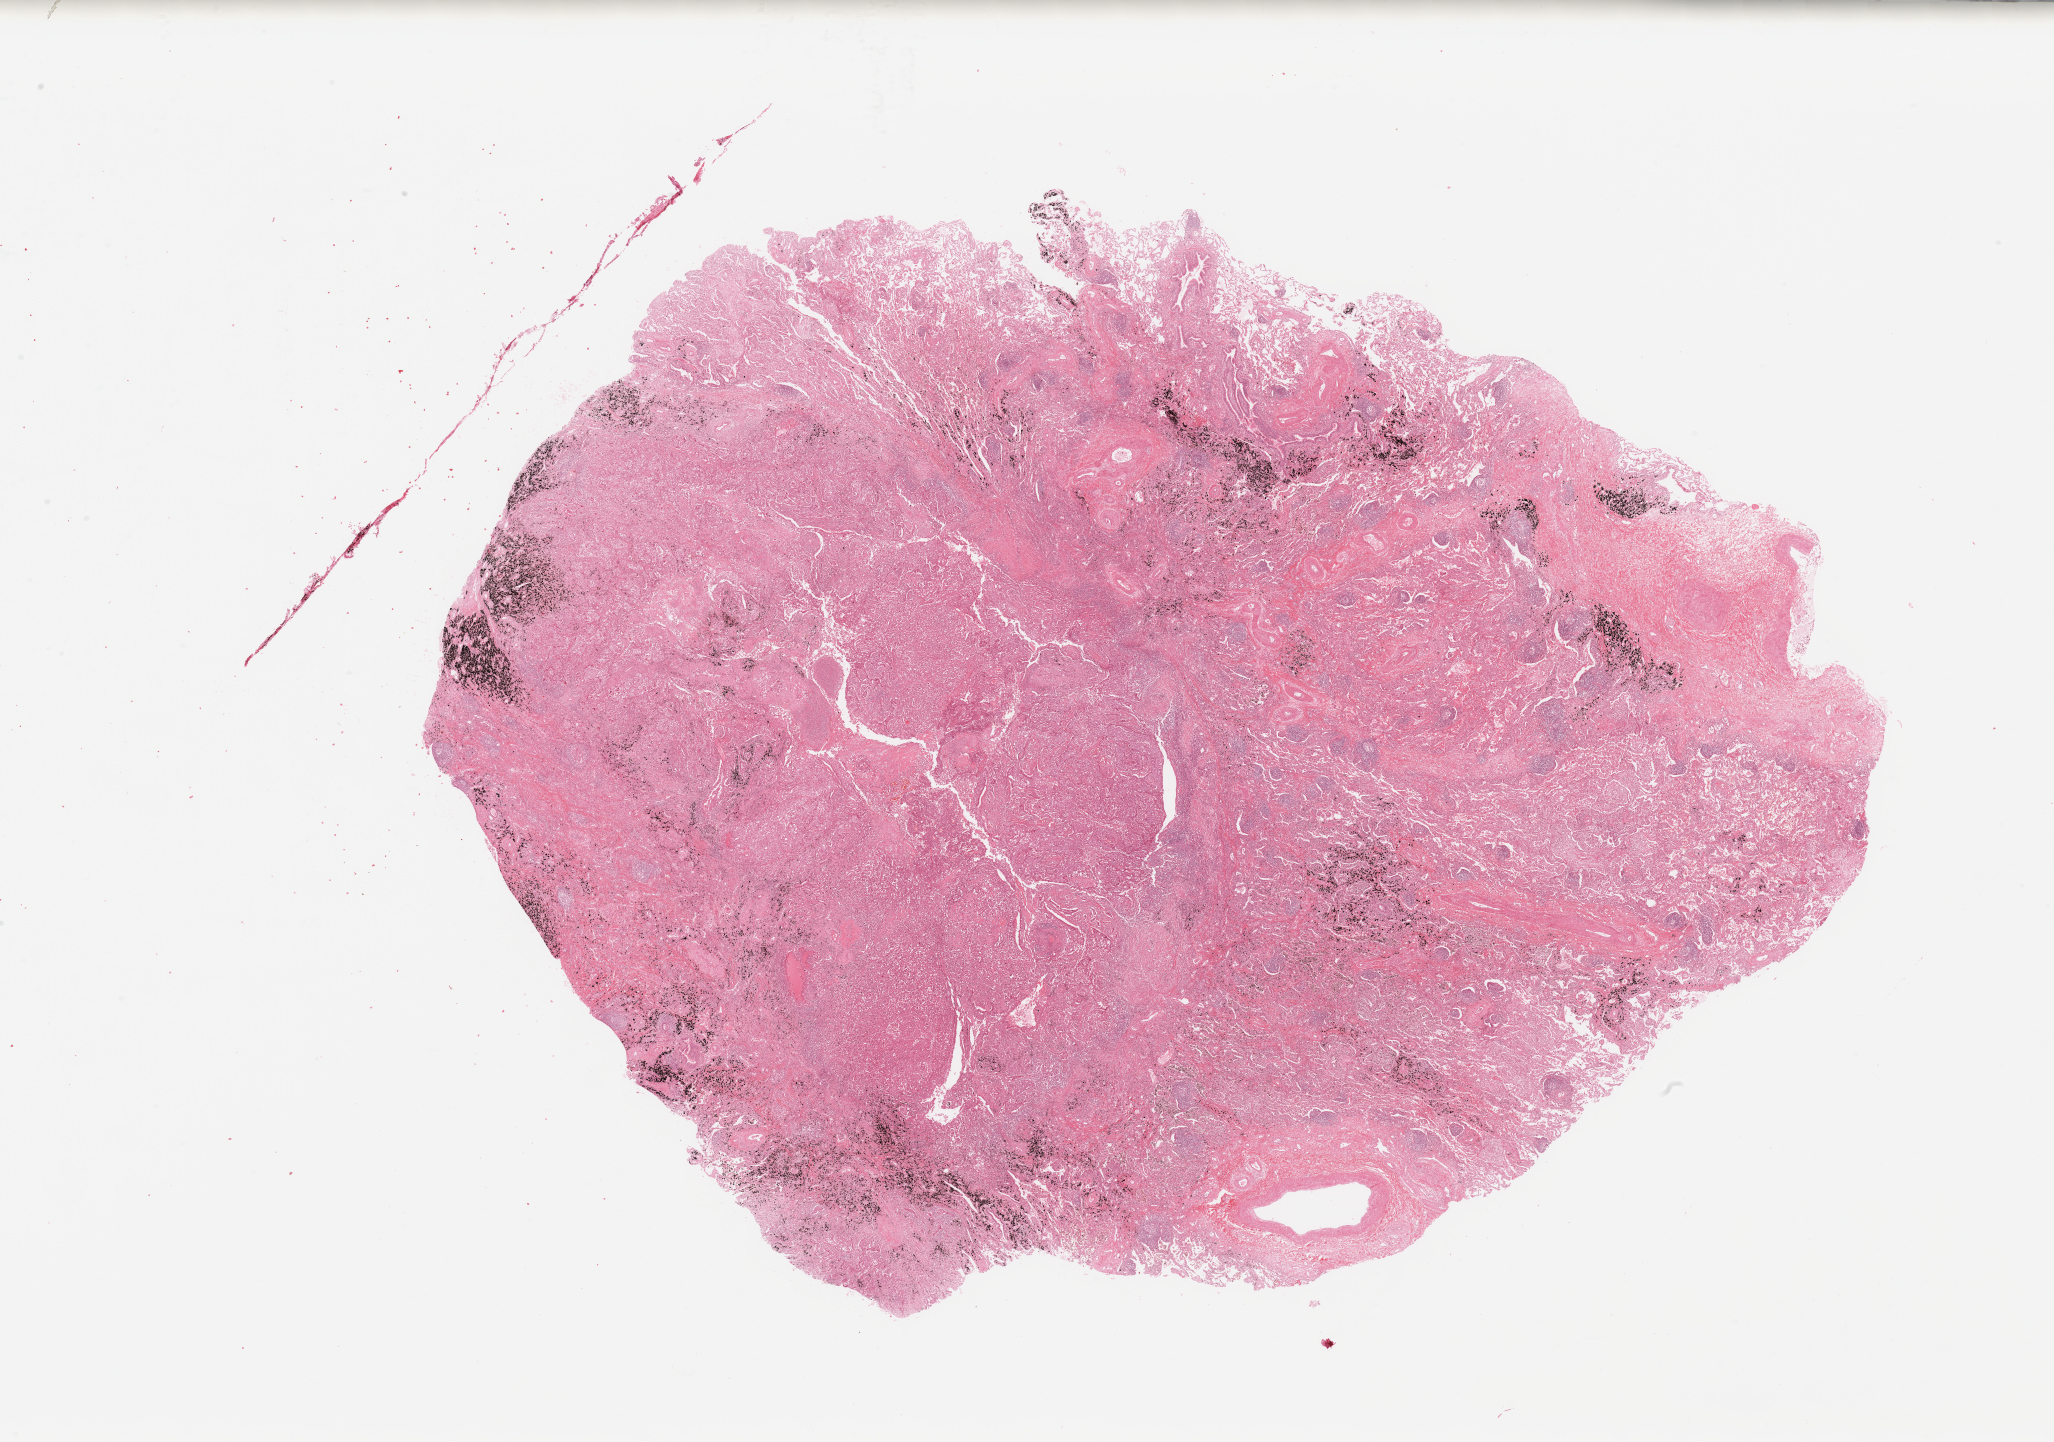
Whole-slide histology image, H&E — shown as a low-resolution overview of the whole scanned area (about 32.5 x 22.8 mm, from a 20x scan); lung, tumour tissue. Patient: male, age 54 years.
Diagnosis: Adenocarcinoma, NOS.